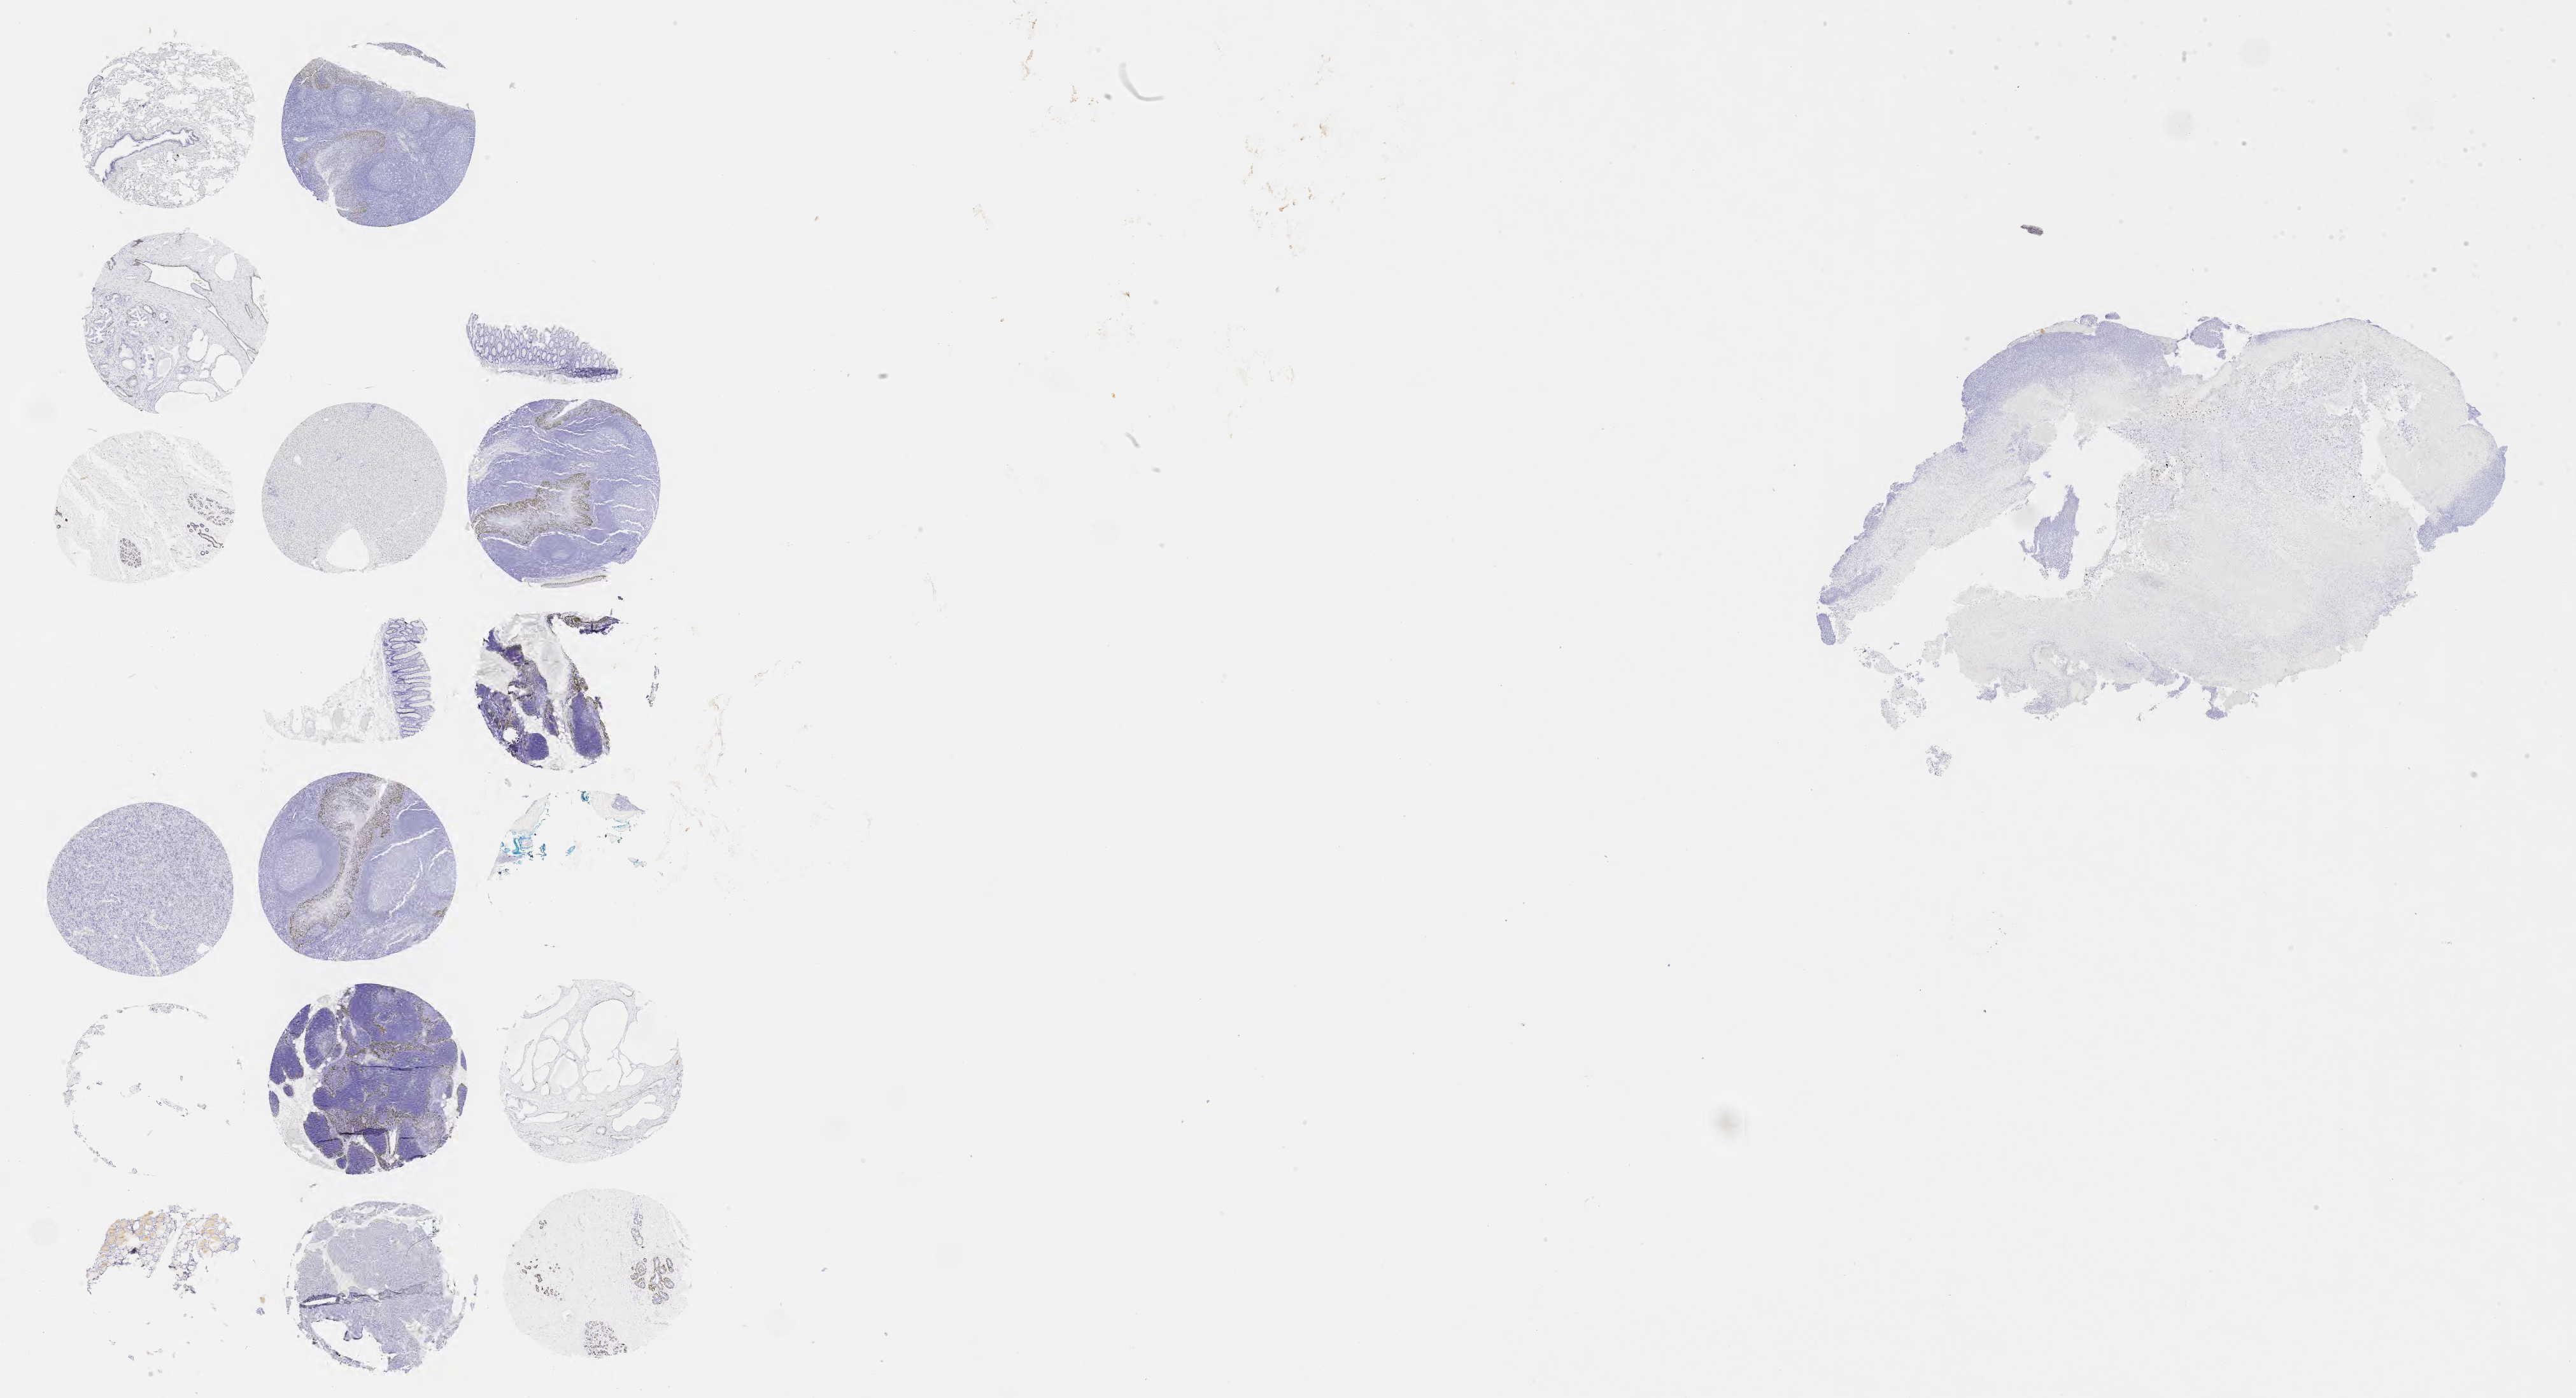
Whole-slide image, immunohistochemical stain for p40 — low-resolution overview of the scanned area, about 32.7 x 17.7 mm; specimen: tumor tissue; site: cervix. Patient female; age 62 years.
- diagnosis: Squamous cell carcinoma, large cell, nonkeratinizing, NOS